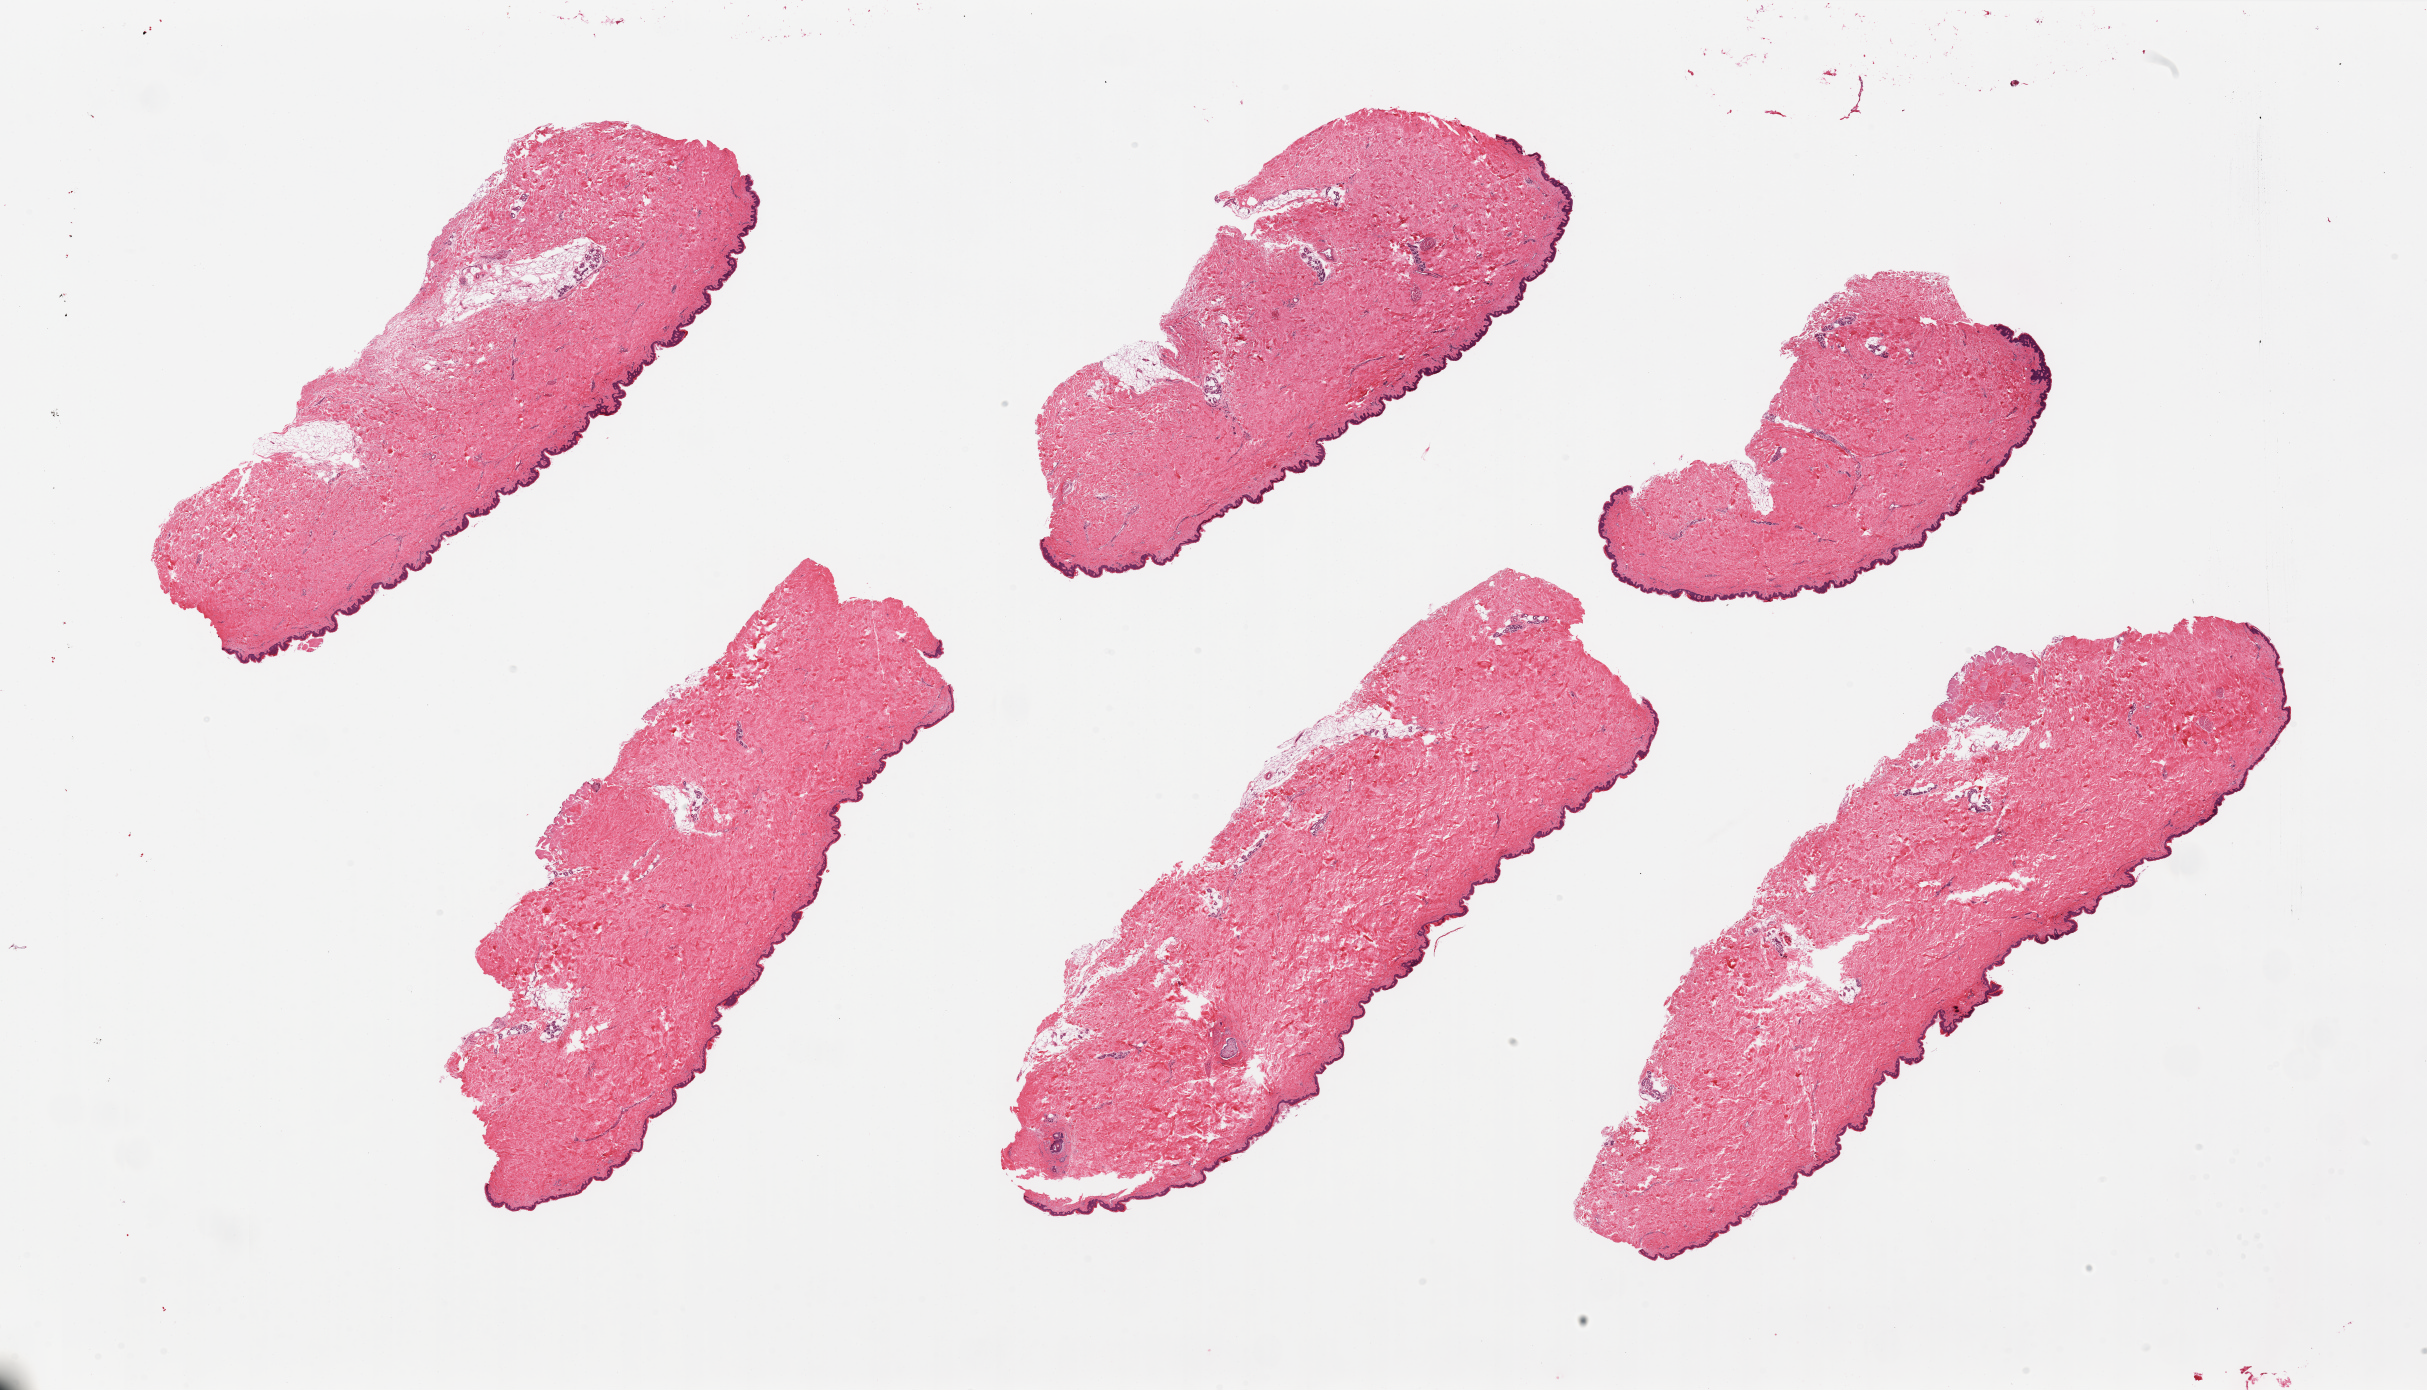
Digitized H&E-stained section, brightfield — whole scanned area (about 38.4 x 22.0 mm) shown as a low-resolution overview. PAXgene-fixed, paraffin-embedded tissue. Sampled site (target tissue): skin of suprapubic region. Tissue donor sample. Female donor.
Reviewer comment on this tissue sample: 6 pieces, well trimmed.